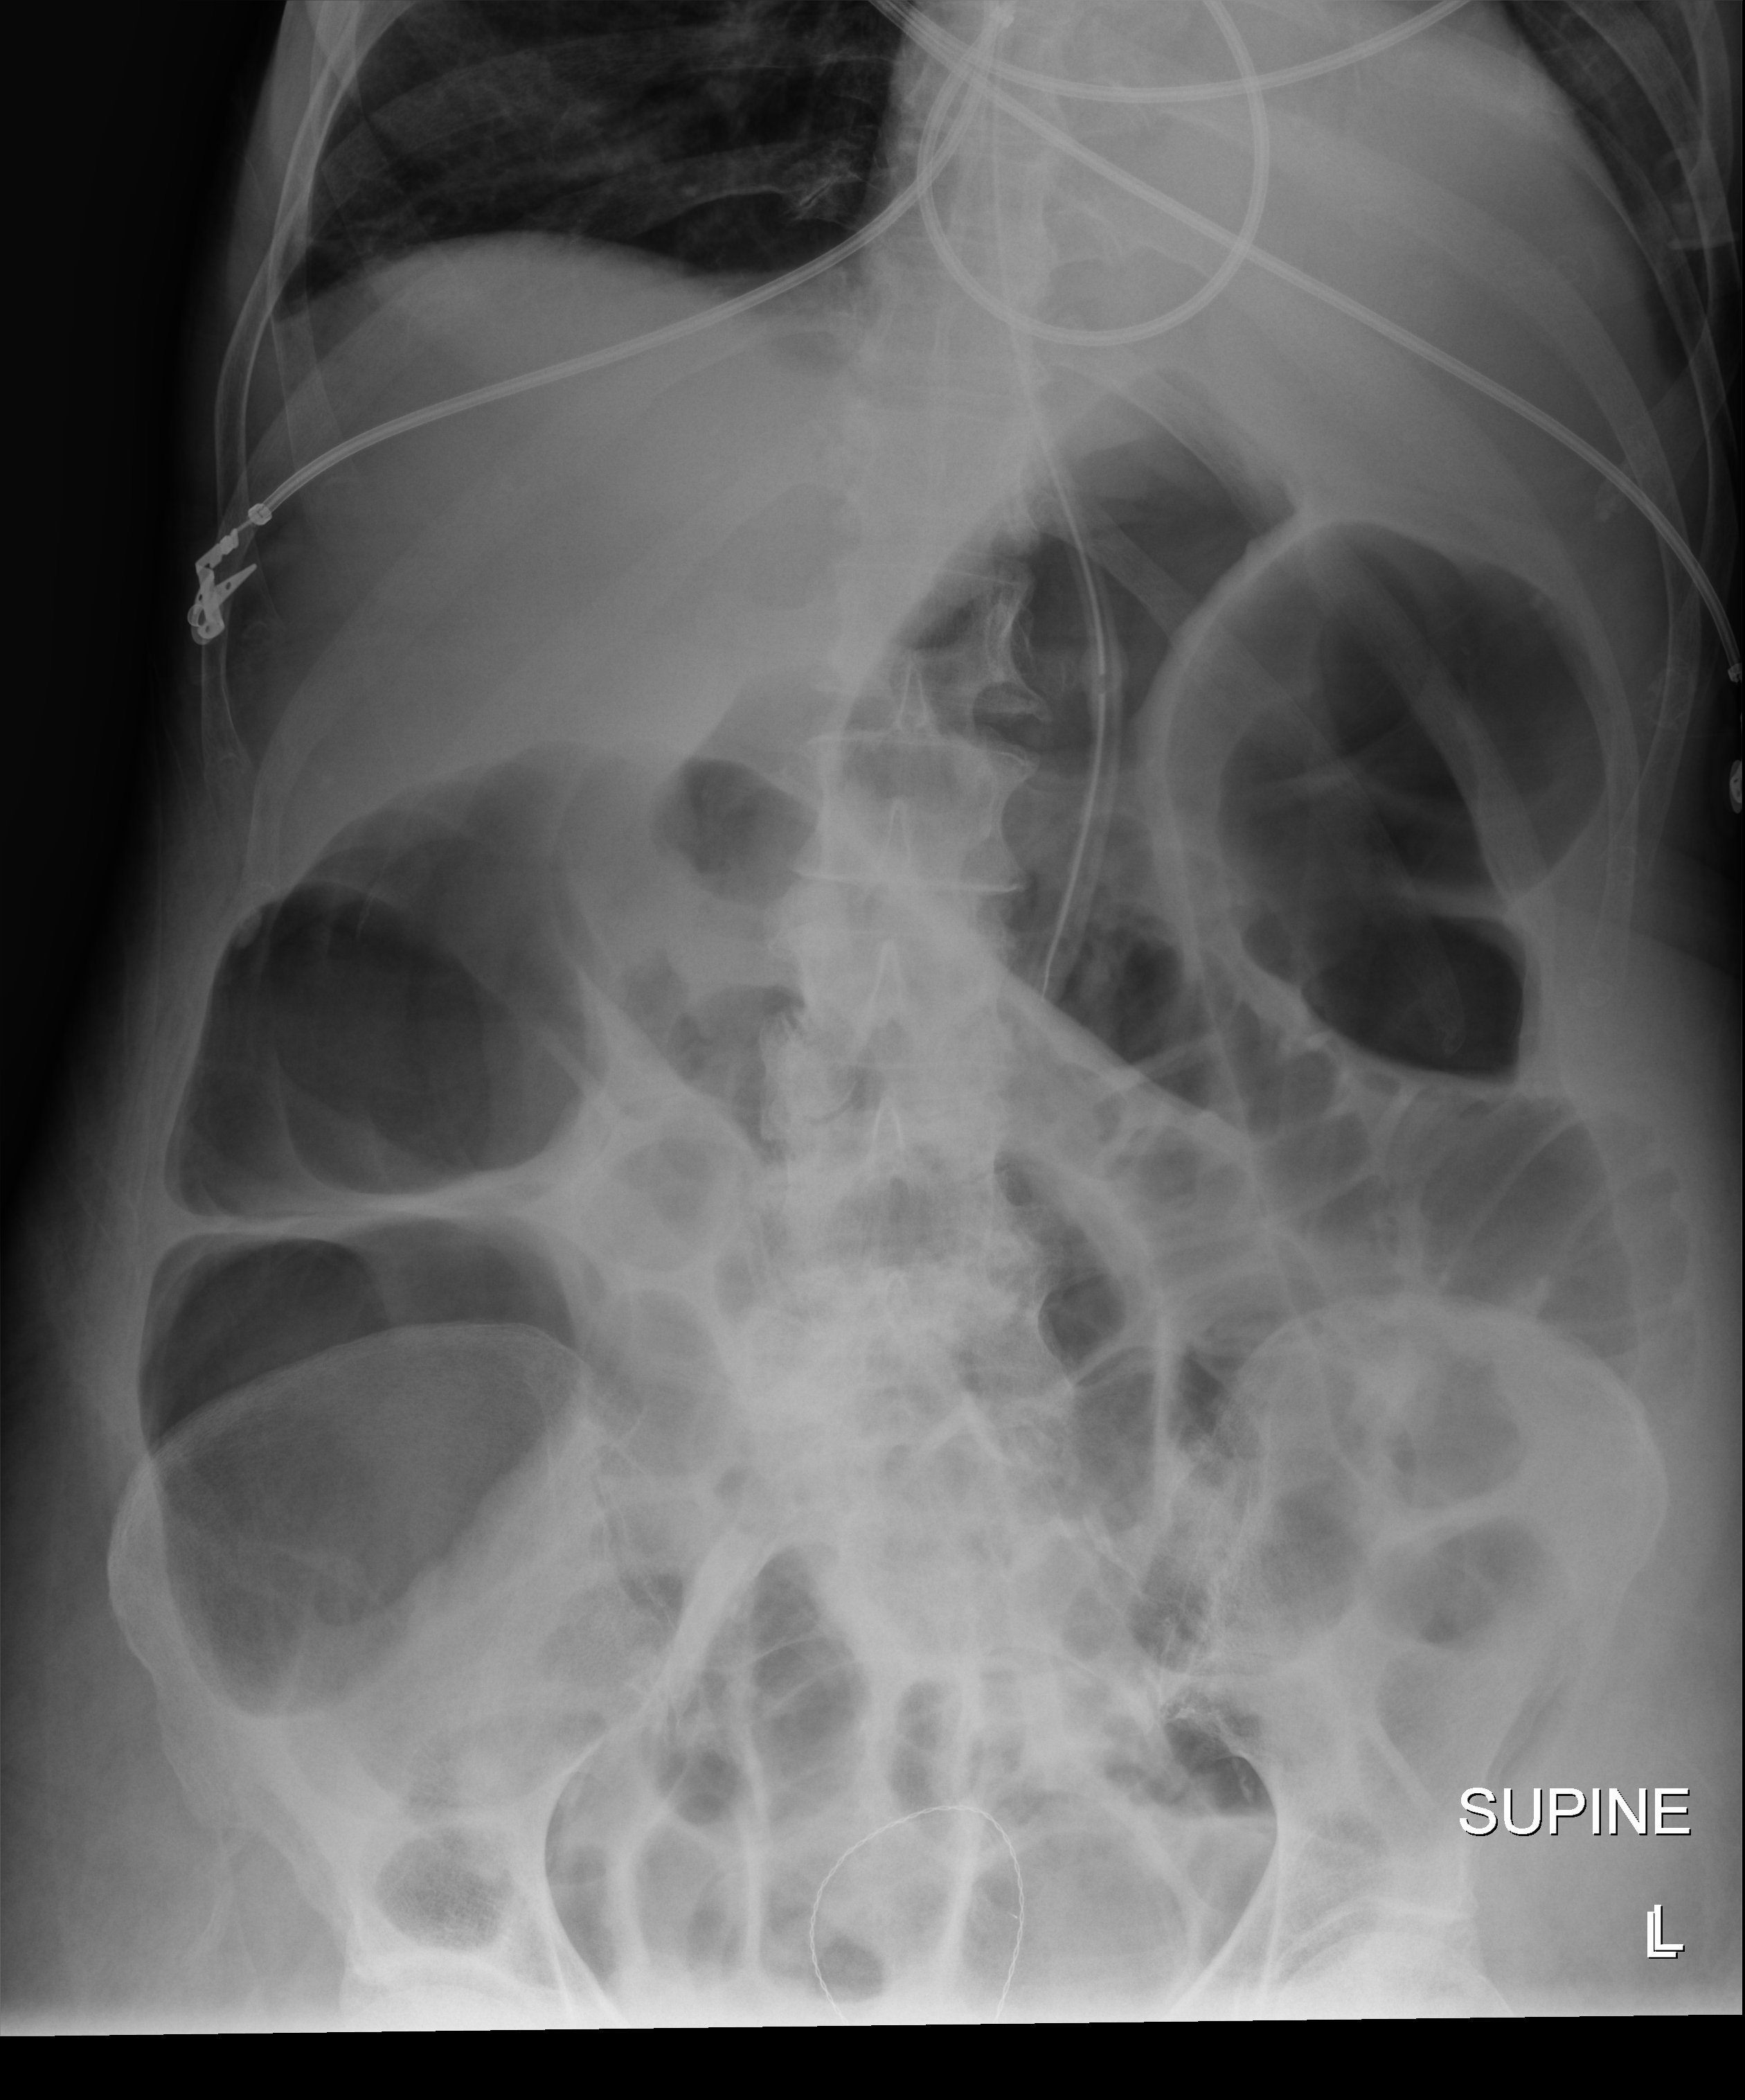
Bedside abdomen radiograph (digital radiography); anteroposterior (AP) projection. Patient hospitalised with COVID-19; female, aged 60–74 years.
Admission-level facts for this patient (not findings on this image; timing relative to this image not recorded): mechanically ventilated during this hospital stay: yes; admitted to intensive care during this hospital stay: yes.